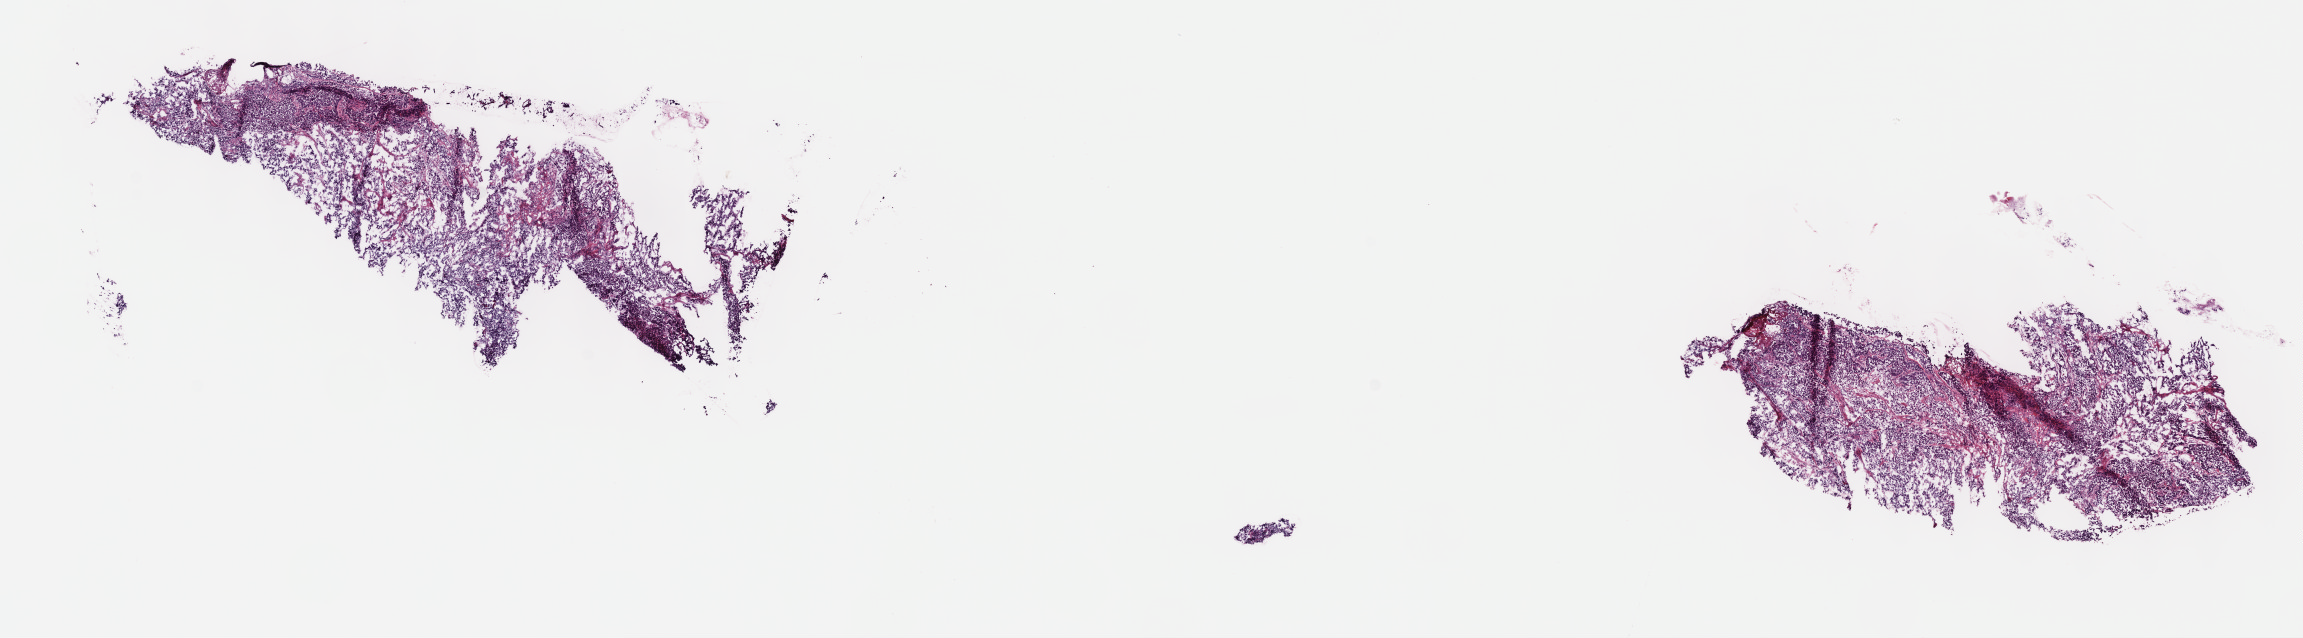
Digitized H&E tissue section (whole slide), a low-resolution overview of the entire scanned area, about 18.6 x 5.2 mm (from a 40x scan); frozen section from the top of the tissue portion; primary tumour sample from the cervix. Patient: female, age at initial diagnosis 35 years. Histologic grade: G2 (moderately differentiated). Composition of this section per pathologist review: tumour cells 96%, tumour nuclei 75%, normal cells 0%, stromal cells 0%, necrosis 4%. Inflammatory infiltration, as recorded: lymphocyte infiltration 2%, monocyte infiltration 0%, neutrophil infiltration 0%.
FIGO stage: IB2. Diagnosis: Adenocarcinoma, endocervical type (cervix uteri).